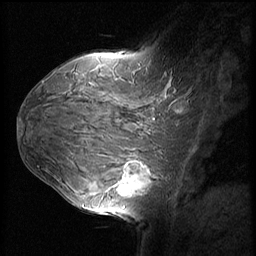
Breast MRI (dynamic contrast-enhanced), one sagittal slice. Position 37 of 60 along the scan axis. Dynamic contrast-enhanced series, image 2 of 3 at this slice position (ordered by acquisition). 1.5 T. TE 4.2 ms, TR 8.9 ms. 2.5 mm slice thickness. 256 × 256 image matrix, field of view 220 × 220 mm. Patient: female, 37 years. Case-level facts recorded for this patient, not image findings: setting: breast cancer imaged before/during neoadjuvant chemotherapy; receptor status: triple-negative.
Annotated regions visible in this slice (semi-automatically segmented with operator editing):
- analysis volume of interest (the breast-tissue region the enhancement analysis was run in; not a lesion): bounding box [x1, y1, x2, y2] px = [114, 153, 159, 206]
- tumour enhancement mask (voxels above the 140 % enhancement threshold inside the analysis volume of interest): [118, 162, 151, 196]